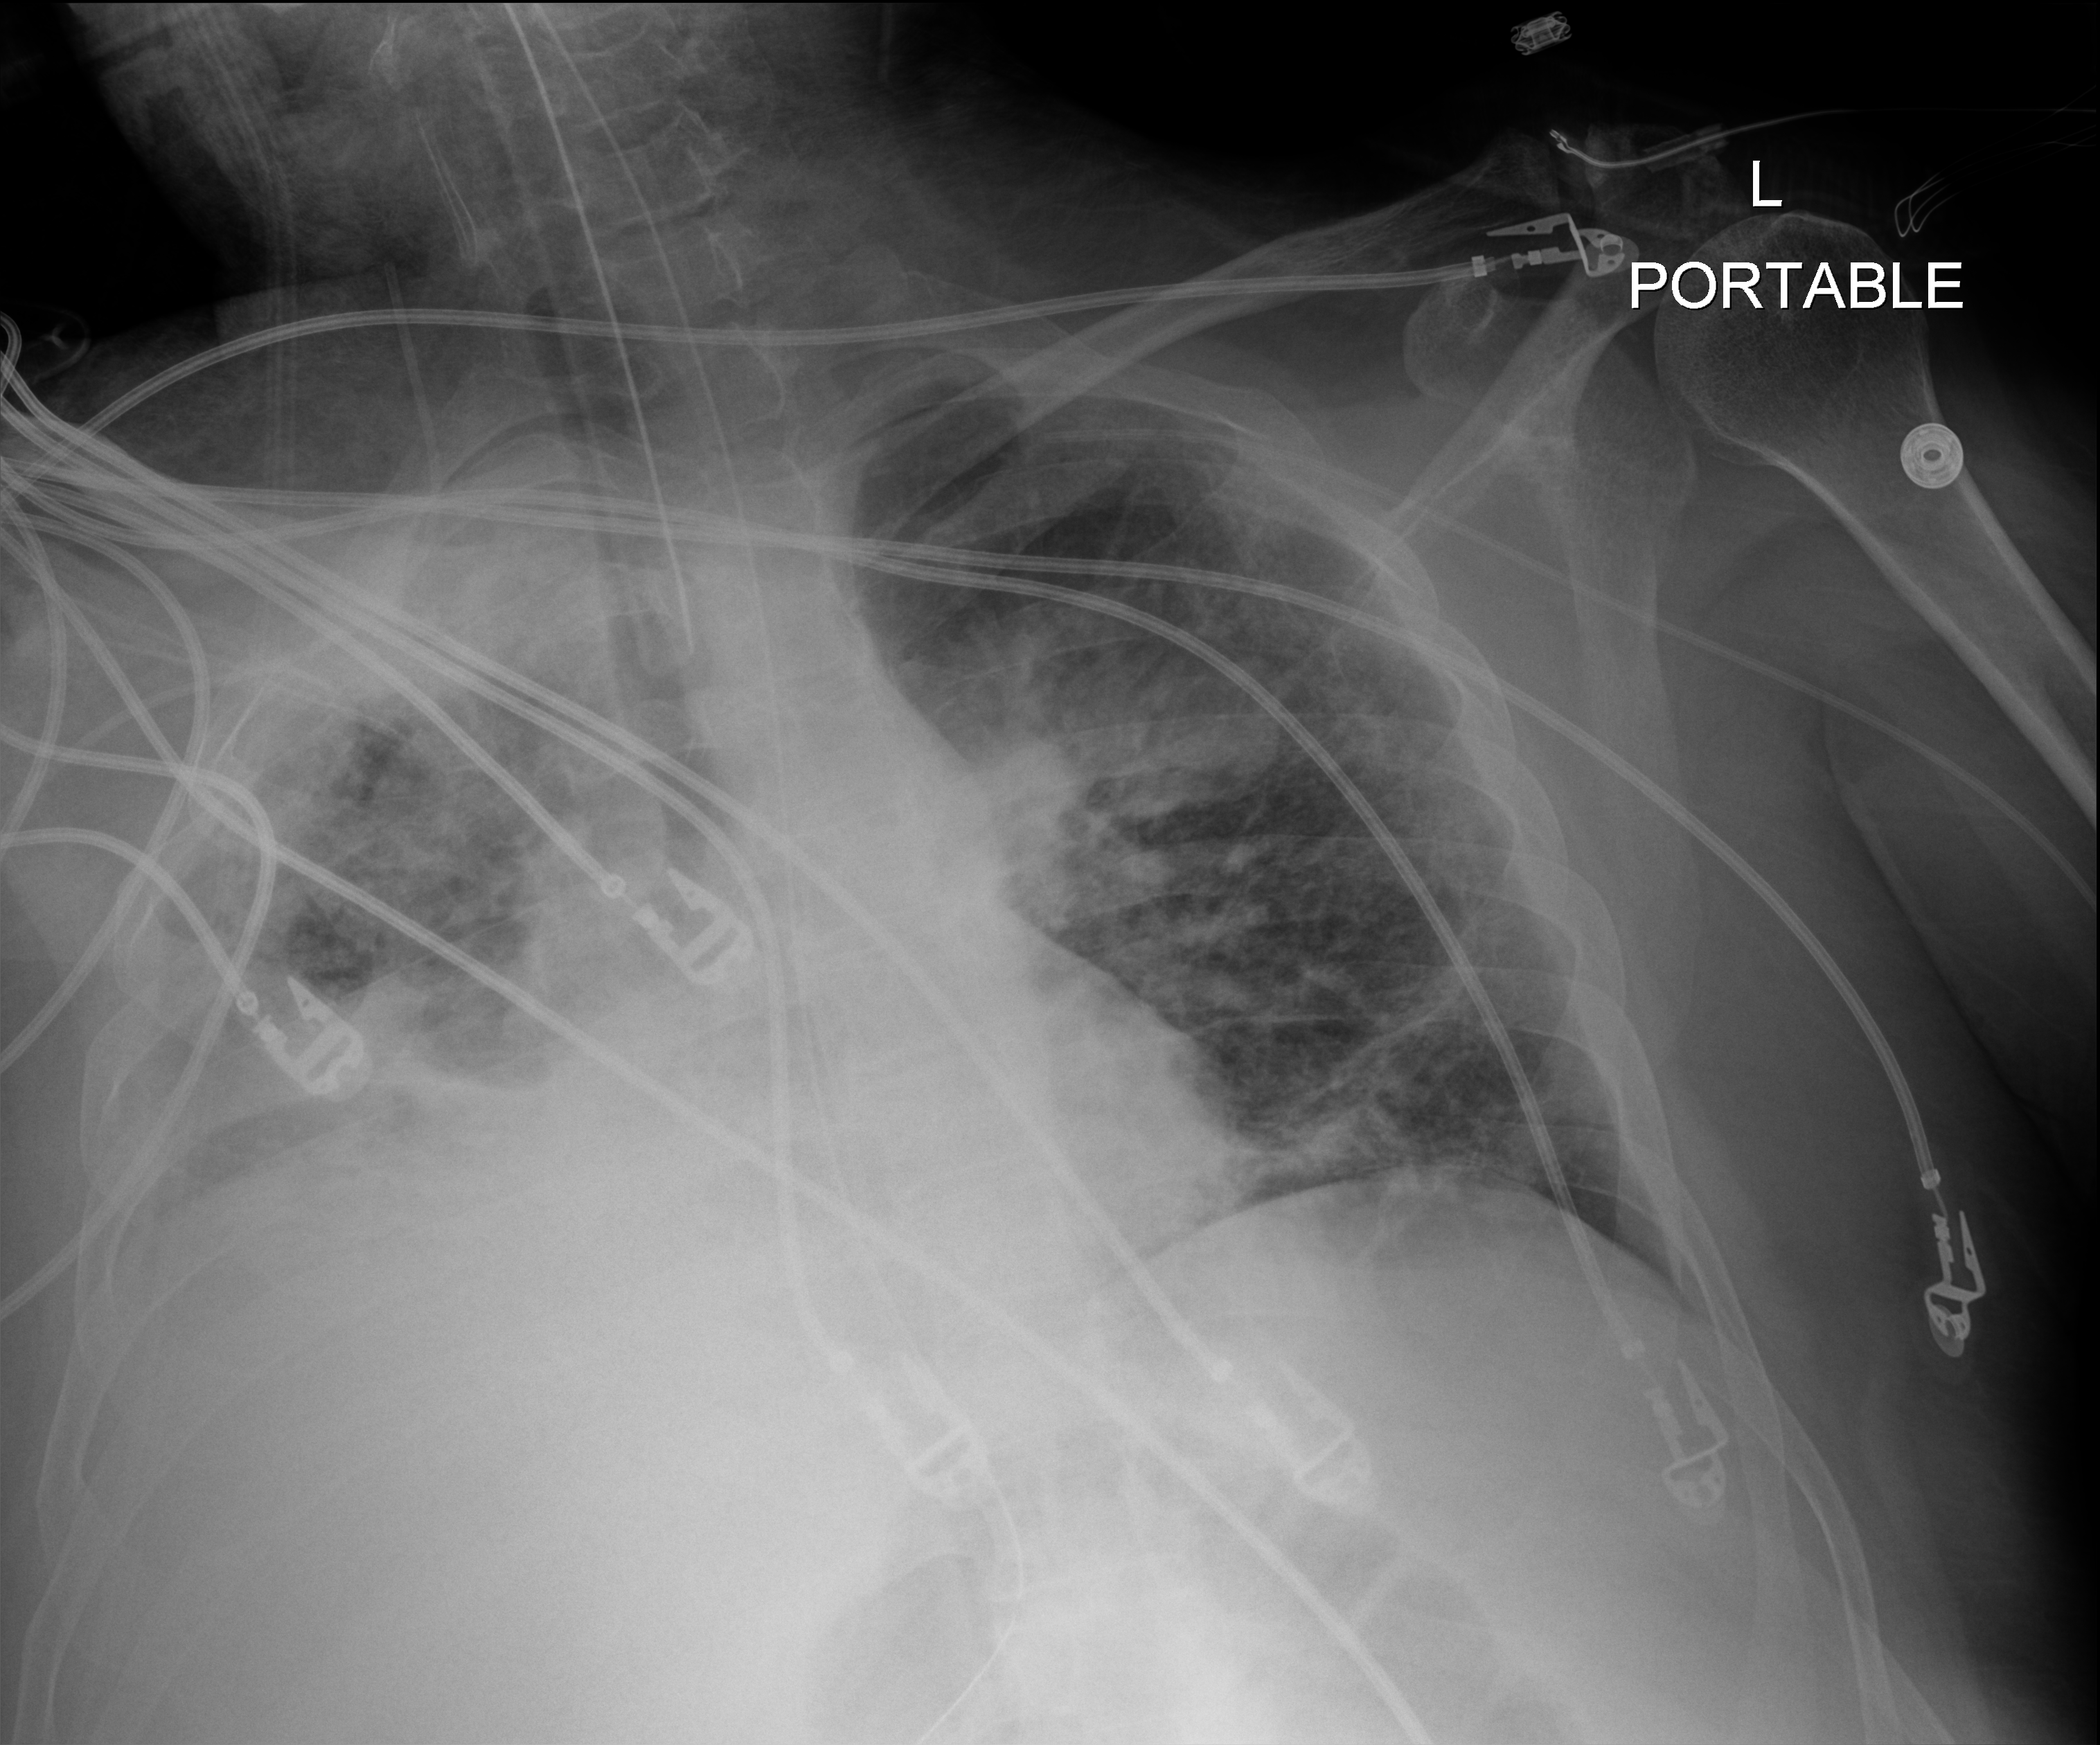
Chest X-ray. Patient hospitalised with COVID-19, aged 18–59 years.
From the hospital-stay record, not from the radiograph (when in the stay this image was taken is not recorded): smoking status (admission record): never; admitted to intensive care during this hospital stay: yes; mechanically ventilated during this hospital stay: yes.